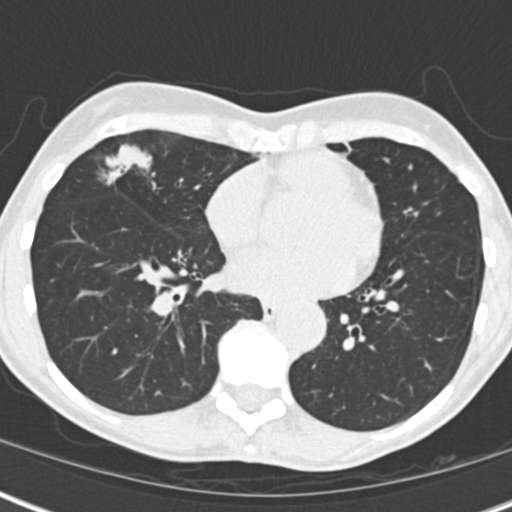
Low-dose screening chest CT, one axial slice. Slice 70 of 173 in the series (ordered by position). Reconstruction kernel B30f. Lung window (W 1500 / L -600 HU). 512 × 512 image matrix.
Annotated regions visible in this slice (manually delineated by an expert):
- lesion 1 (tumor, middle lobe of right lung): bounding box [x1, y1, x2, y2] px = [107, 147, 150, 182]